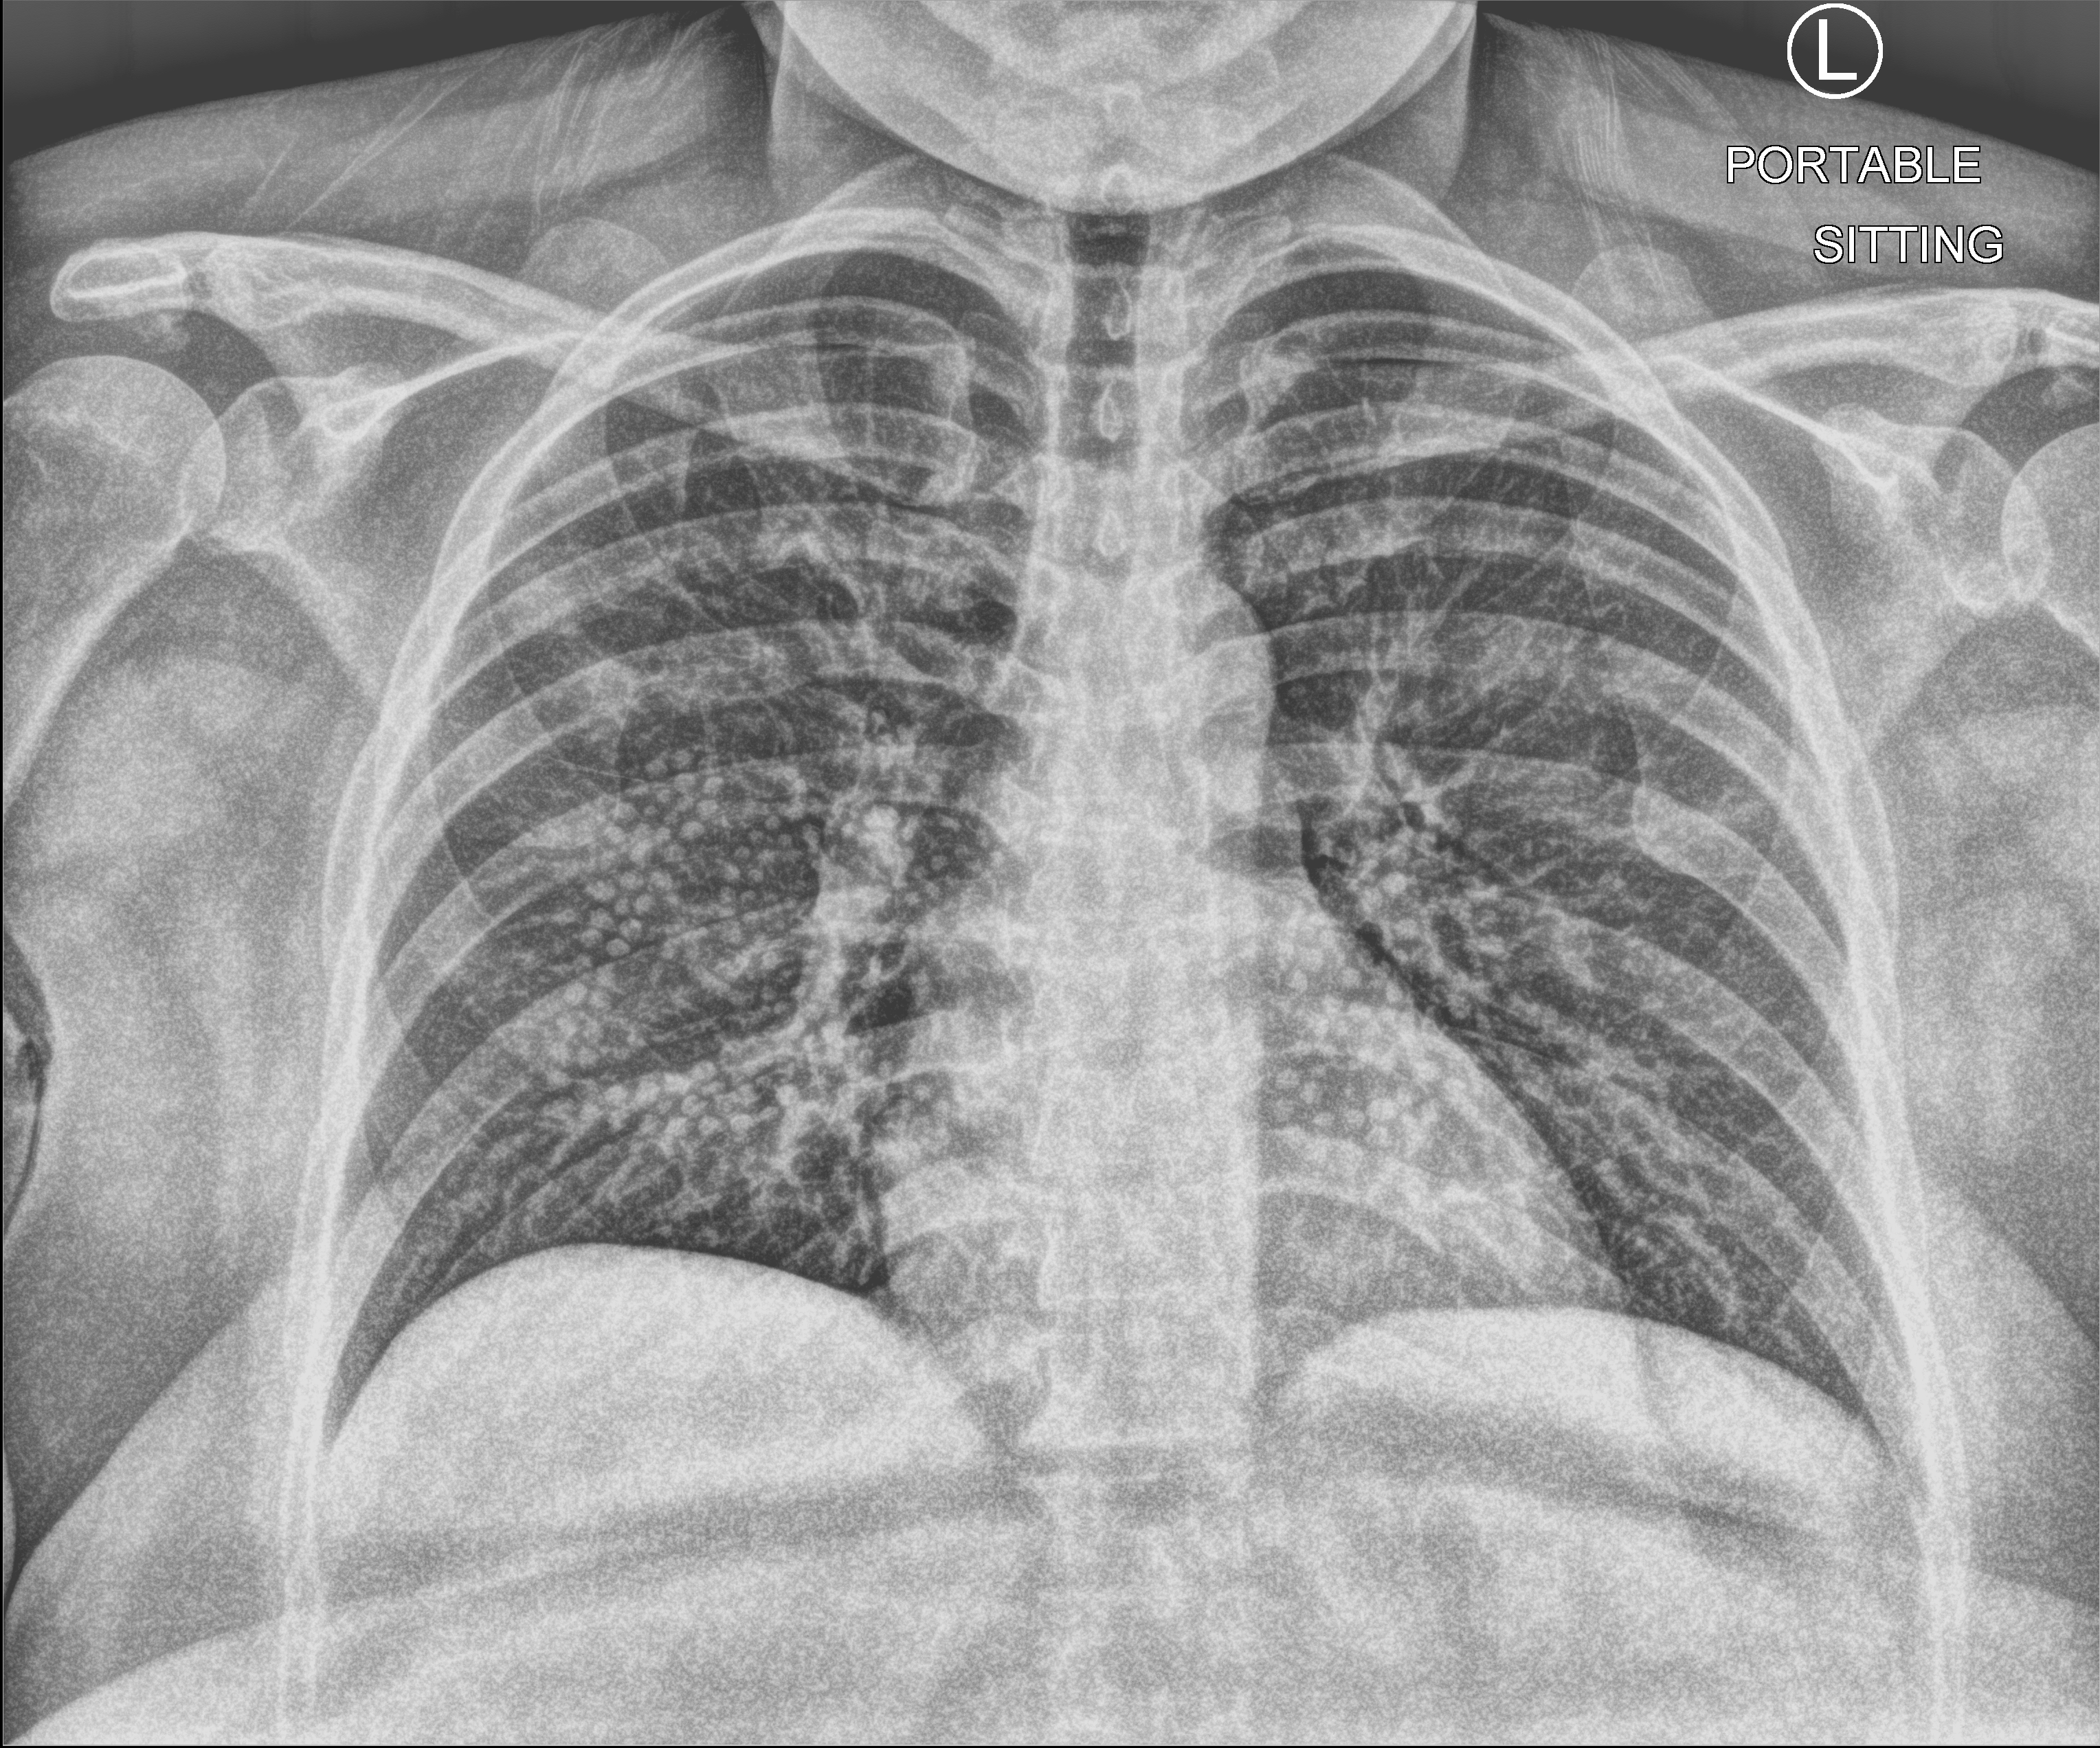
Chest X-ray (portable), anteroposterior (AP) projection. Female patient hospitalised with COVID-19, age 18–59 years.
From the hospital-stay record, not from the radiograph (when in the stay this image was taken is not recorded): admitted to intensive care during this hospital stay: no; mechanically ventilated during this hospital stay: no.